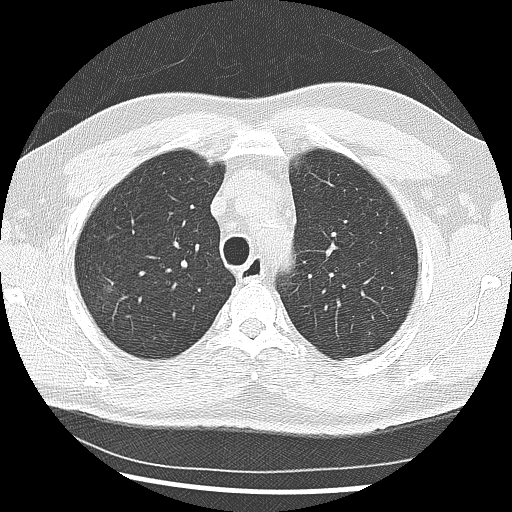
Low-dose screening chest CT, one axial slice. Reconstruction kernel LUNG. Lung window (W 1500 / L -600 HU). 2.5 mm slice thickness. 512 × 512 image matrix, field of view 340 × 340 mm.
Annotated regions visible in this slice (outlined manually by an expert reader):
- lesion 1 (tumor, upper lobe of right lung): bounding box [x1, y1, x2, y2] px = [108, 285, 113, 293]